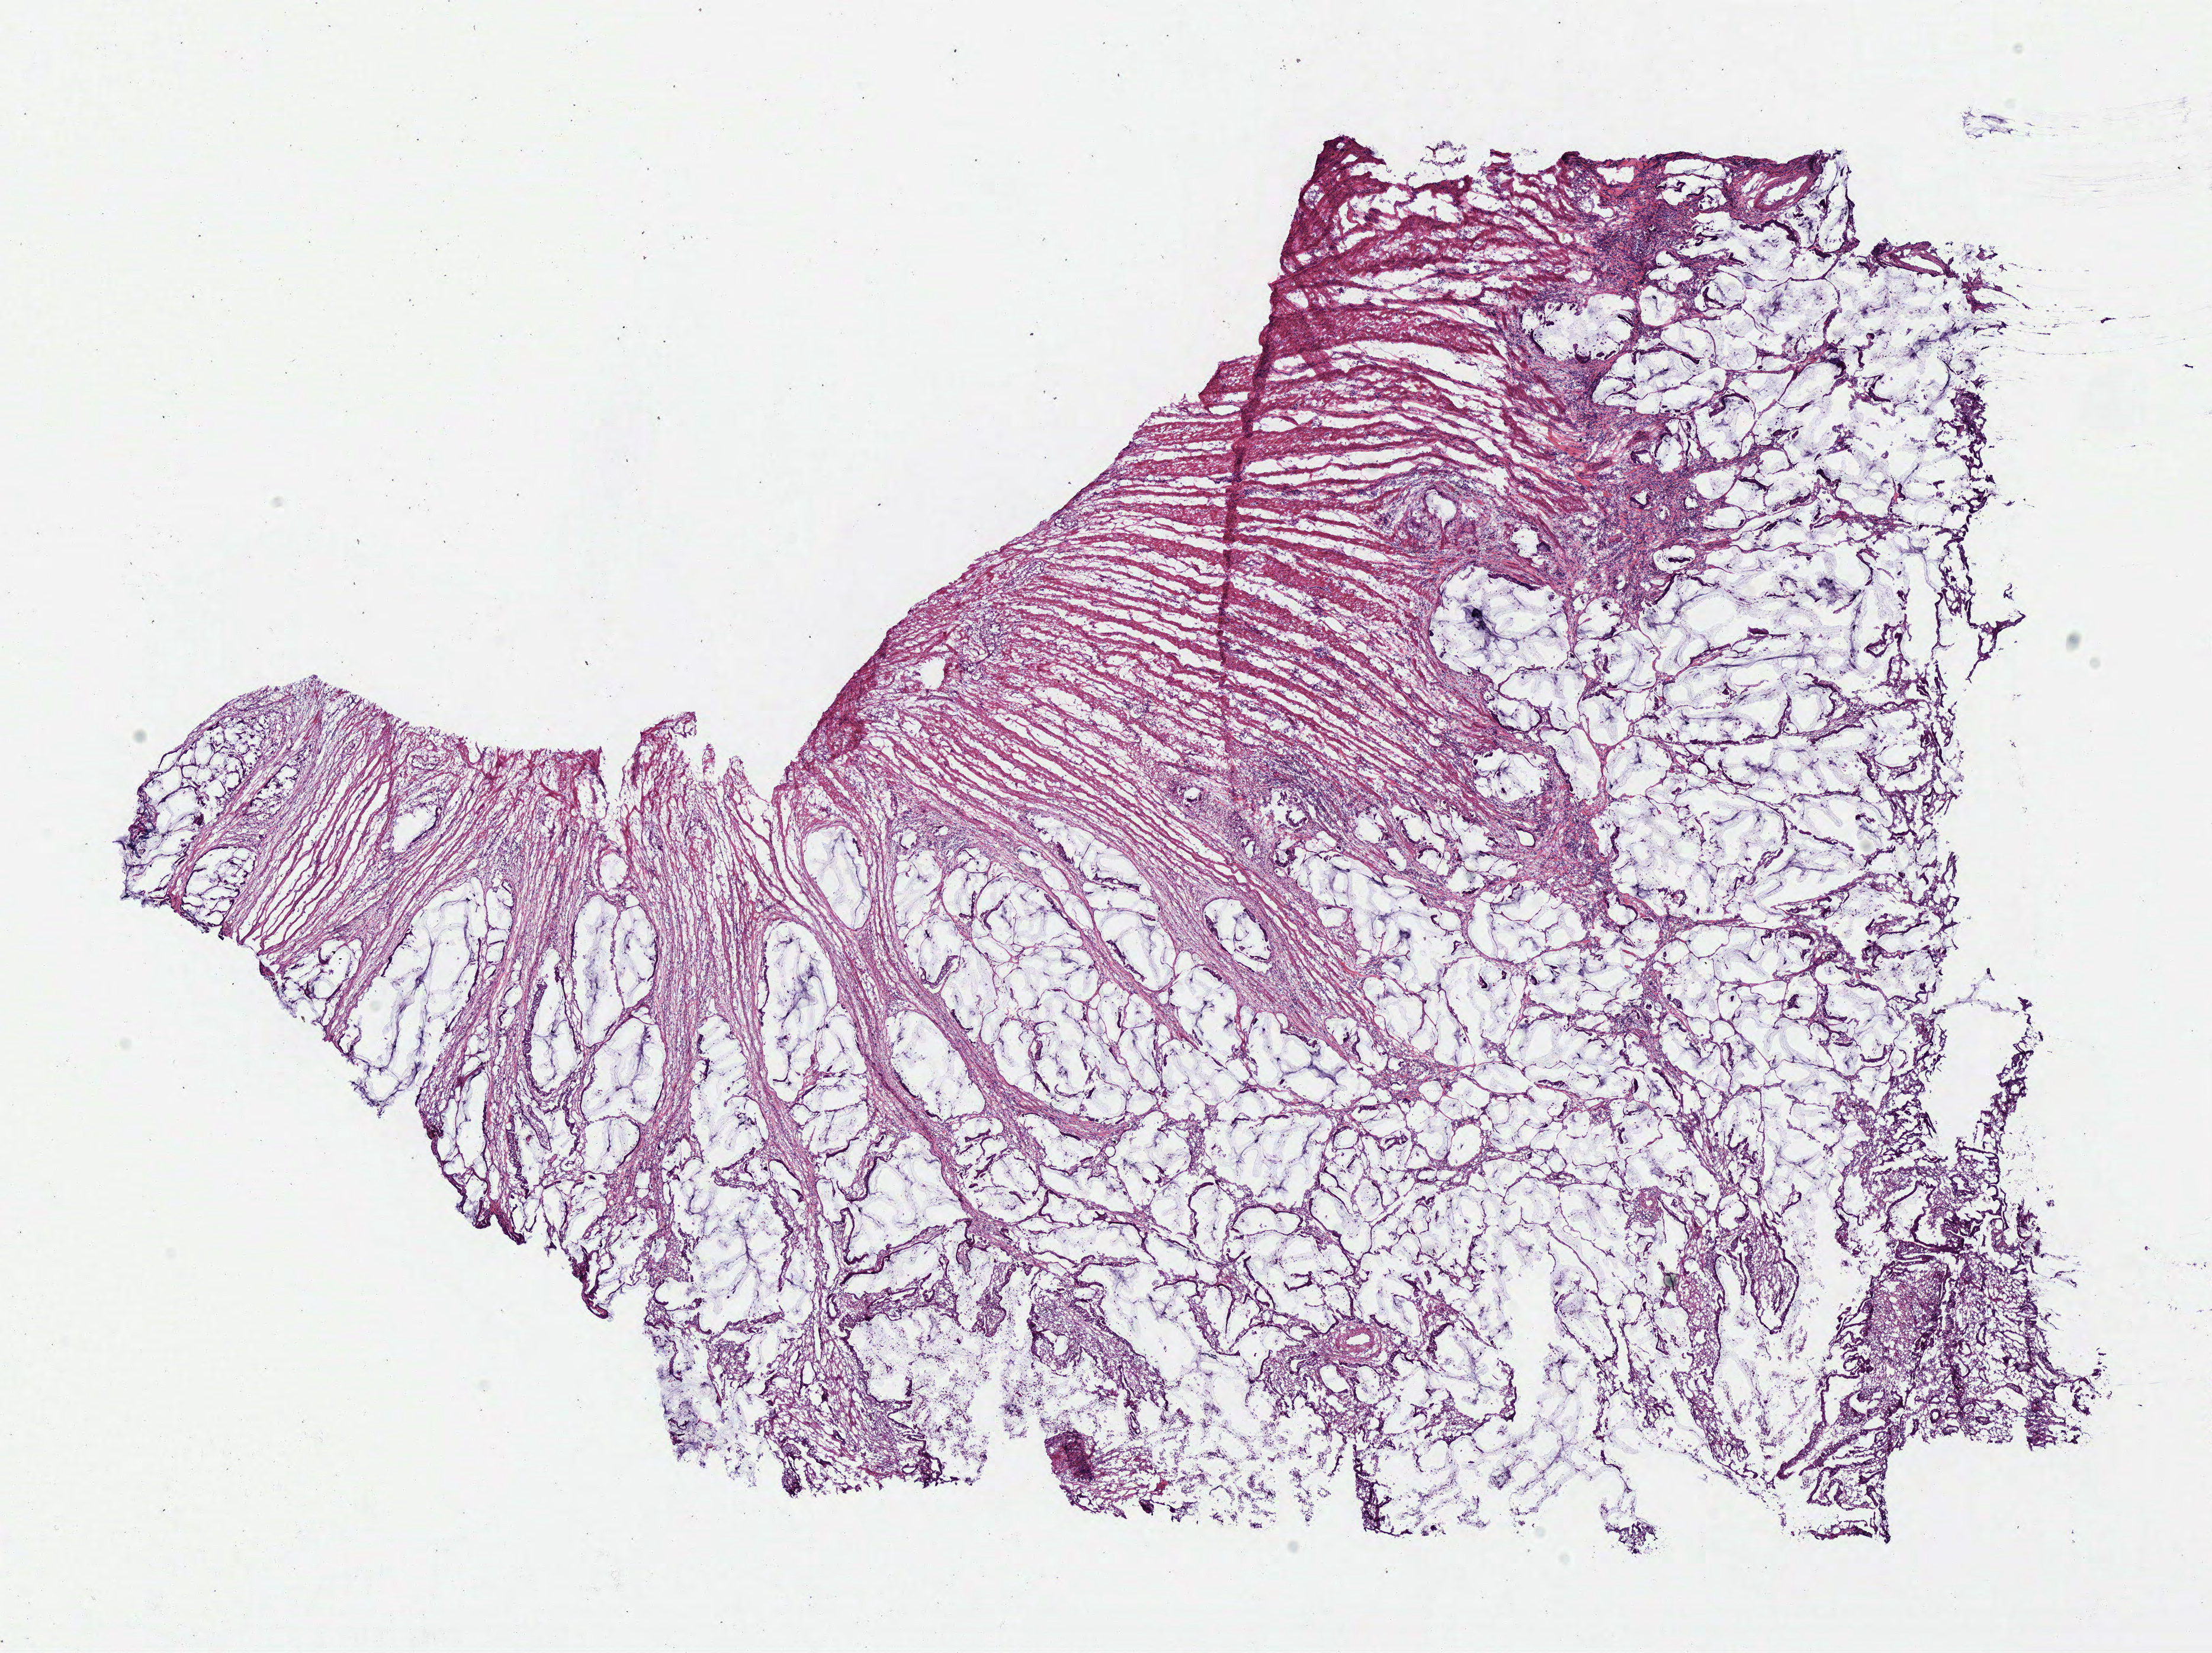
Digitized H&E tissue section (whole slide) — a low-resolution overview of the entire scanned area, about 14.7 x 11.0 mm, frozen section from the bottom of the tissue portion, primary tumour sample from the colon. Female patient. Pathologist review of this section (percent, as recorded): tumour cells 72%, tumour nuclei 80%, normal cells 3%, stromal cells 25%, necrosis 0%.
- diagnosis: Mucinous adenocarcinoma (cecum)
- lymph nodes positive (case pathology): 0 of 15 examined
- TNM: T3 N0 M0
- AJCC pathologic stage: IIA (6th edition)